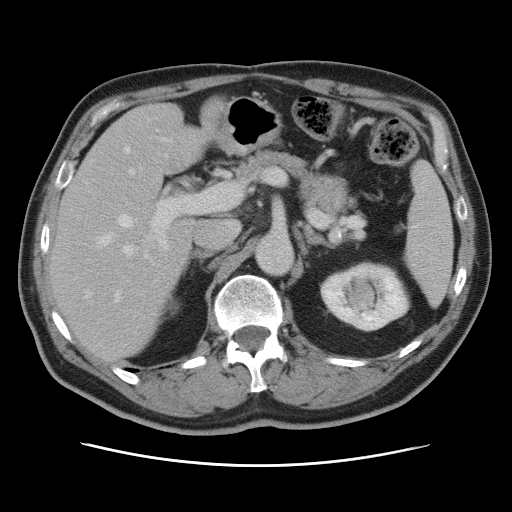
Contrast-enhanced abdominal CT, one axial slice. Position 46 of 80 along the scan axis. 120 kVp. Intravenous contrast given. Soft-tissue window (W 400 / L 40 HU). 5 mm slice thickness. 512 × 512 image matrix, field of view 370 × 370 mm. Male patient, age 69 years. Case-level facts recorded for this patient, not image findings: diagnosis: colorectal cancer liver metastases, imaged before liver resection; multiple liver metastases: no; largest metastasis: 5 cm; chemotherapy before resection: no.
Annotated regions visible in this slice (outlined manually by an expert reader):
- hepatic veins: bounding box (x1, y1, x2, y2) in pixels: (99, 147, 148, 301)
- liver: (47, 104, 211, 358)
- planned liver remnant (the part of the liver to remain after resection): (47, 127, 210, 357)
- portal vein (with intrahepatic branches): (122, 139, 205, 257)